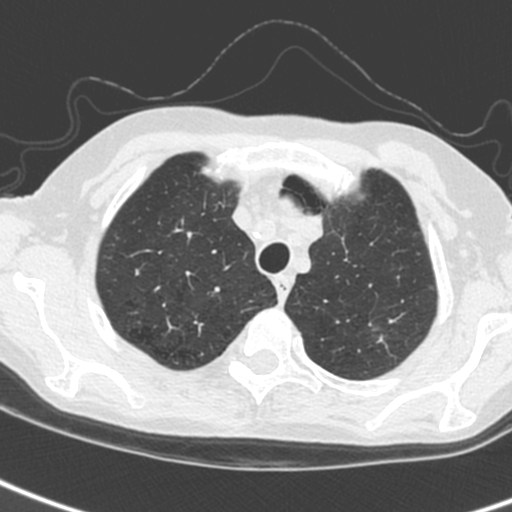
Chest CT (low-dose screening protocol), one axial image. First (baseline) screen. Lung window (W 1500 / L -600 HU). 1.3 mm slice thickness. Standard (soft-tissue) reconstruction kernel (C). Slice 31 of 242 in the series. Female participant, aged 61 years at enrolment. Current smoker at enrolment.
- Lesion marked by an expert reader, box from (x=356, y=310) to (x=413, y=354) px.
- The screening reader recorded 2 non-calcified nodules or masses ≥4 mm on this exam (left upper lobe, left upper lobe); which of them this box marks is not recorded.
- Official screen result: positive, change unspecified: nodule(s) >= 4 mm or enlarging nodule(s), mass(es), or other non-specific abnormalities suspicious for lung cancer.
- Lung cancer was diagnosed 29 days after this screen: small cell carcinoma, NOS, left upper lobe, stage IV (AJCC 6th edition).